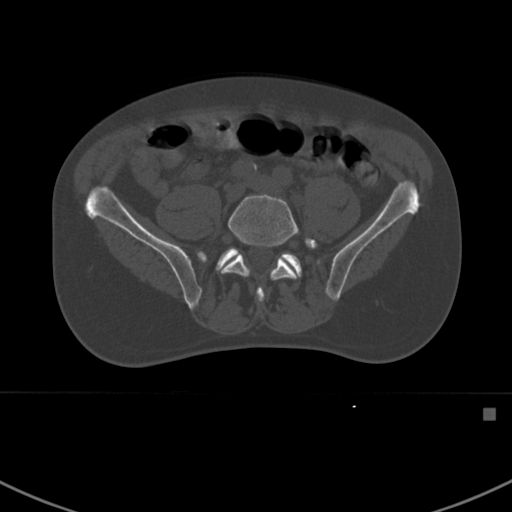
CT including the spine, one axial slice; position 215 of 412 along the scan axis; reconstruction kernel Br40s; 120 kVp; bone window (W 1800 / L 400 HU); 1.5 mm slice thickness; 512 × 512 image matrix. Patient: male, 59 years. Case-level facts recorded for this patient, not image findings: primary cancer: prostate.
Outlined on this slice (semi-automatically segmented with operator editing):
- L5 vertebra: bounding box <221,194,317,303> (left, top, right, bottom; pixels)